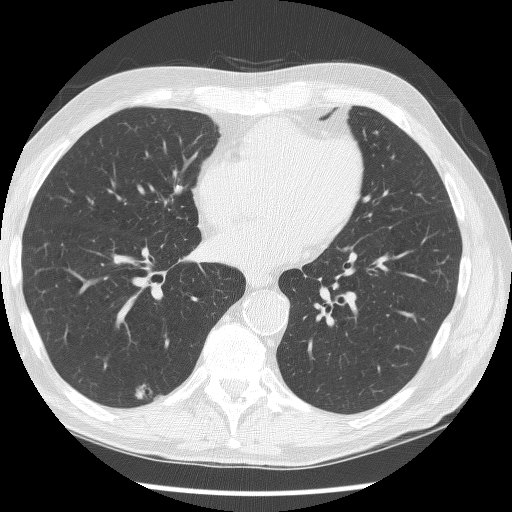
Chest CT (low-dose screening protocol), one axial image, baseline annual screen, lung window (W 1500 / L -600 HU), 2.5 mm slice thickness, lung (sharp) reconstruction kernel (BONE), 512 × 512 image matrix, field of view 340 × 340 mm. Male participant, aged 62 years at enrolment.
- Expert reader's lesion annotation, box from (x=124, y=381) to (x=162, y=411) px.
- The screening reader recorded 2 non-calcified nodules or masses ≥4 mm on this exam; which of them this box marks is not recorded.
- Official screen result: positive, change unspecified: nodule(s) >= 4 mm or enlarging nodule(s), mass(es), or other non-specific abnormalities suspicious for lung cancer.
- Lung cancer was diagnosed 849 days after this screen: adenocarcinoma, NOS, right lower lobe, moderately differentiated (G2), stage IIIB (AJCC 6th edition), 15 mm at pathology.